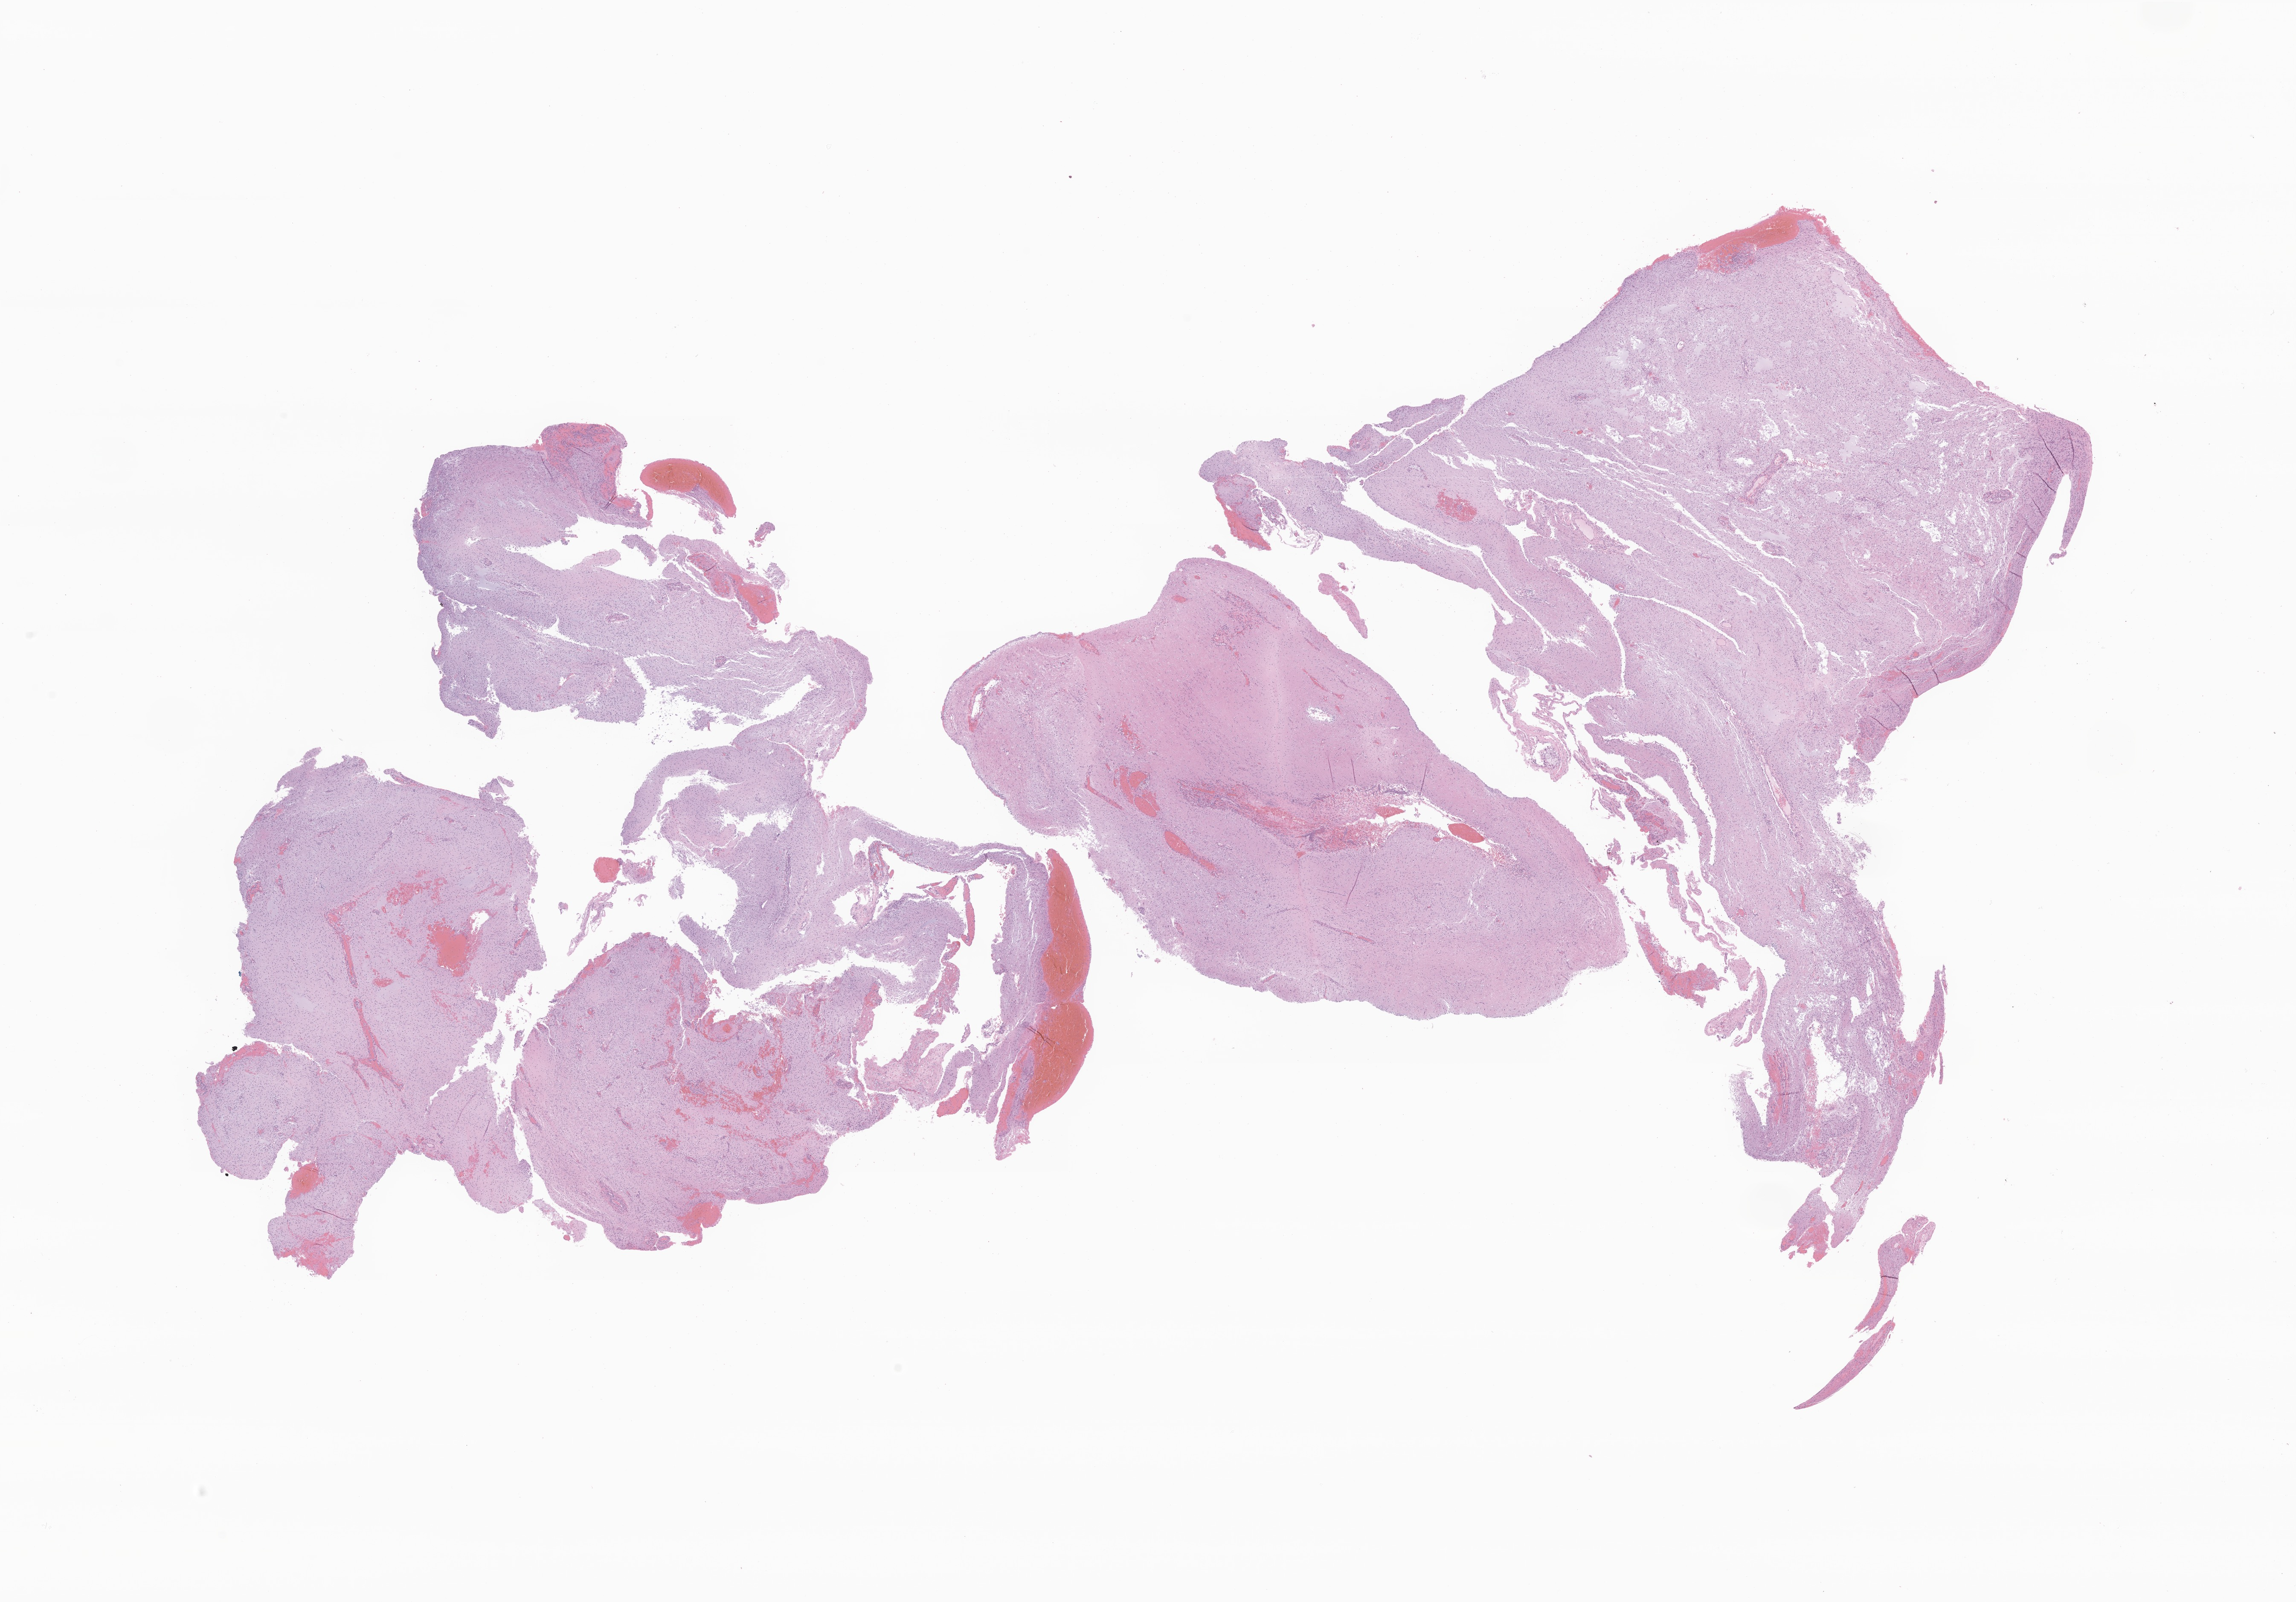
Whole-slide image, haematoxylin and eosin stain of tumor tissue from the brain, shown as a low-resolution overview of the whole scanned area (about 22.7 x 15.8 mm), formalin-fixed, paraffin-embedded (FFPE) tissue. Patient: male, age 73 months.
- diagnosis: Neoplasm, uncertain whether benign or malignant